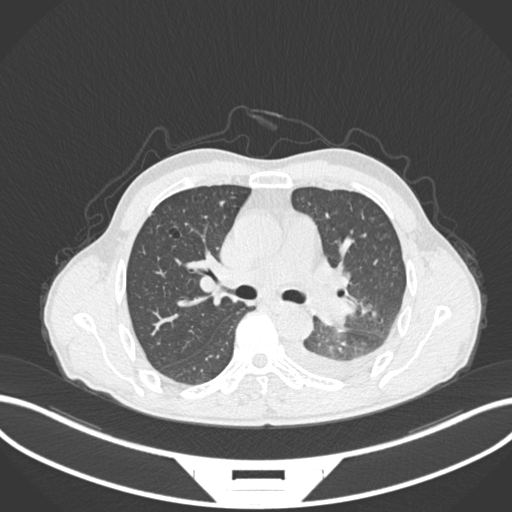
Chest CT, one axial slice; position 154 of 222 along the scan axis; reconstruction kernel B30f; 120 kVp; lung window (W 1500 / L -600 HU); 1 mm slice thickness; 512 × 512 image matrix, field of view 400 × 400 mm. Patient: male, 47 years. From the clinical record (not read from this slice): clinical TNM (as recorded): T3 N1 M1c.
Outlined on this slice (bounding box drawn by a radiologist):
- lung tumour (recorded histology: small cell carcinoma): bounding box <320,294,358,327> (left, top, right, bottom; pixels)